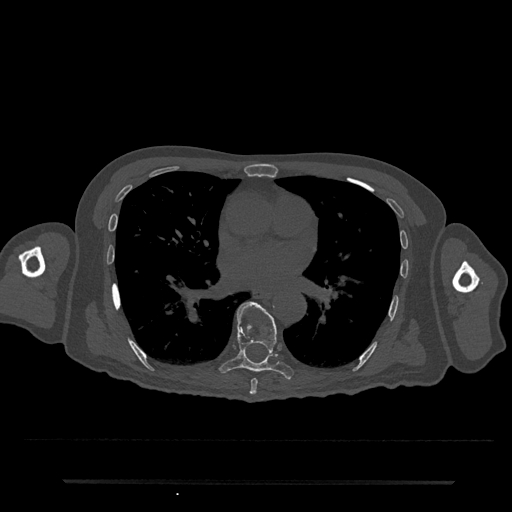
CT including the spine, one axial slice; position 432 of 797 along the scan axis; 120 kVp; bone window (W 1800 / L 400 HU); 0.5 mm slice thickness; 512 × 512 image matrix, field of view 427 × 427 mm. Patient: male, 74 years. Case-level facts recorded for this patient, not image findings: primary cancer: prostate.
Annotated regions visible in this slice (semi-automatically segmented with operator editing):
- T7 vertebra: bounding box (x1, y1, x2, y2) in pixels: (249, 379, 258, 395)
- T8 vertebra: (219, 301, 294, 380)